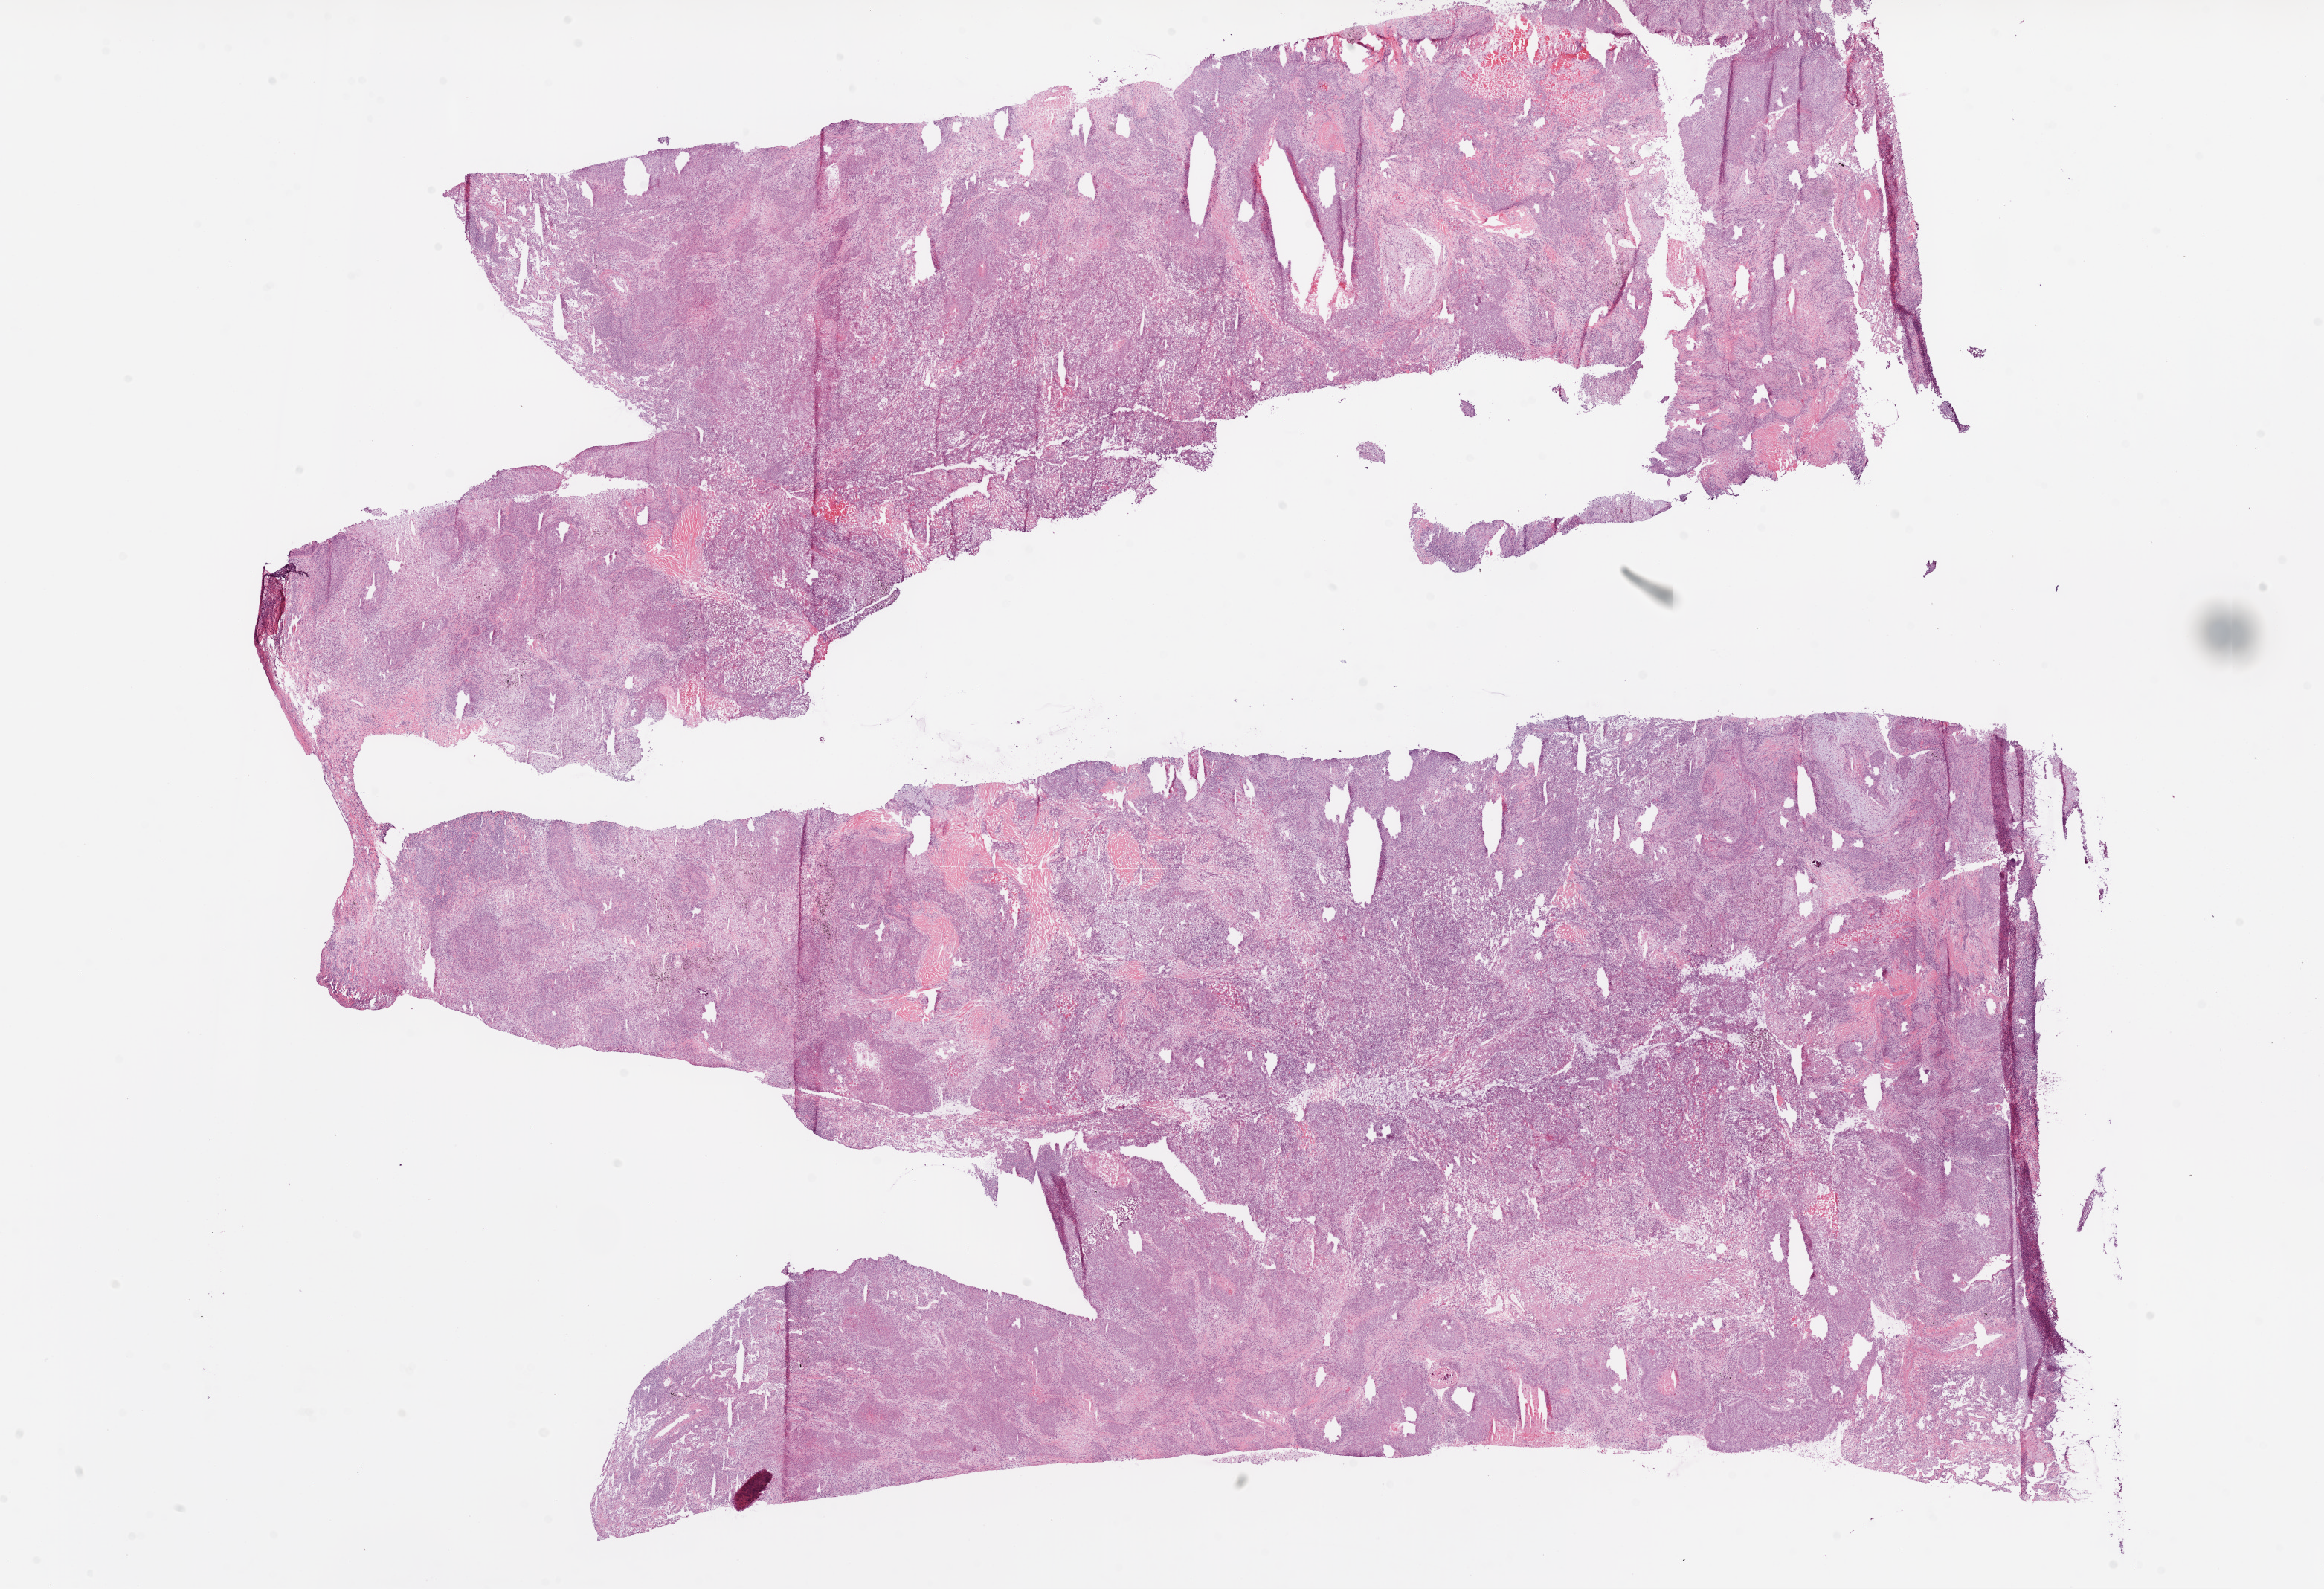
Digitized Hematoxylin and eosin (H&E) stained tissue section (whole slide) — shown as a low-resolution overview of the whole scanned area (about 25.1 x 17.1 mm, slide scanned at 20x). Frozen section. Sample: primary tumour, lung. Female, age 81 years at initial diagnosis. Pathologist review of this section (percent, as recorded): tumour cells 65%, tumour nuclei 75%, normal cells 5%, stromal cells 25%, necrosis 5%.
* AJCC pathologic stage: IIIA
* TNM: T2a N2 M0
* pathologic diagnosis: Squamous cell carcinoma, NOS (lower lobe, lung)